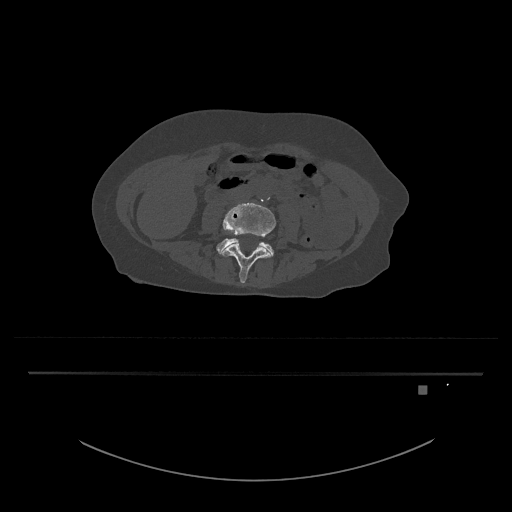
CT including the spine, one axial slice; slice 345 of 797 in the series (ordered by position); reconstruction kernel Br40s/3; 120 kVp; bone window (W 1800 / L 400 HU); 0.5 mm slice thickness; 512 × 512 image matrix, field of view 500 × 500 mm. Female patient, age 57 years. Case-level facts recorded for this patient, not image findings: primary cancer: cervical.
Outlined on this slice (semi-automatically segmented with operator editing):
- L4 vertebra: bounding box (x1, y1, x2, y2) in pixels: (220, 203, 276, 283)